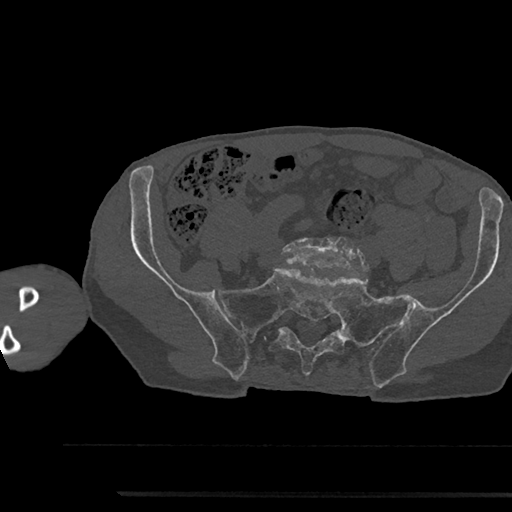
CT including the spine, one axial slice. Position 293 of 797 along the scan axis. 120 kVp. Bone window (W 1800 / L 400 HU). 0.5 mm slice thickness. 512 × 512 image matrix. Patient: male, 79 years. From the clinical record (not read from this slice): primary cancer: prostate.
Structures marked on this image (semi-automatically segmented with operator editing):
- L5 vertebra: bounding box (x1, y1, x2, y2) in pixels: (282, 237, 363, 269)